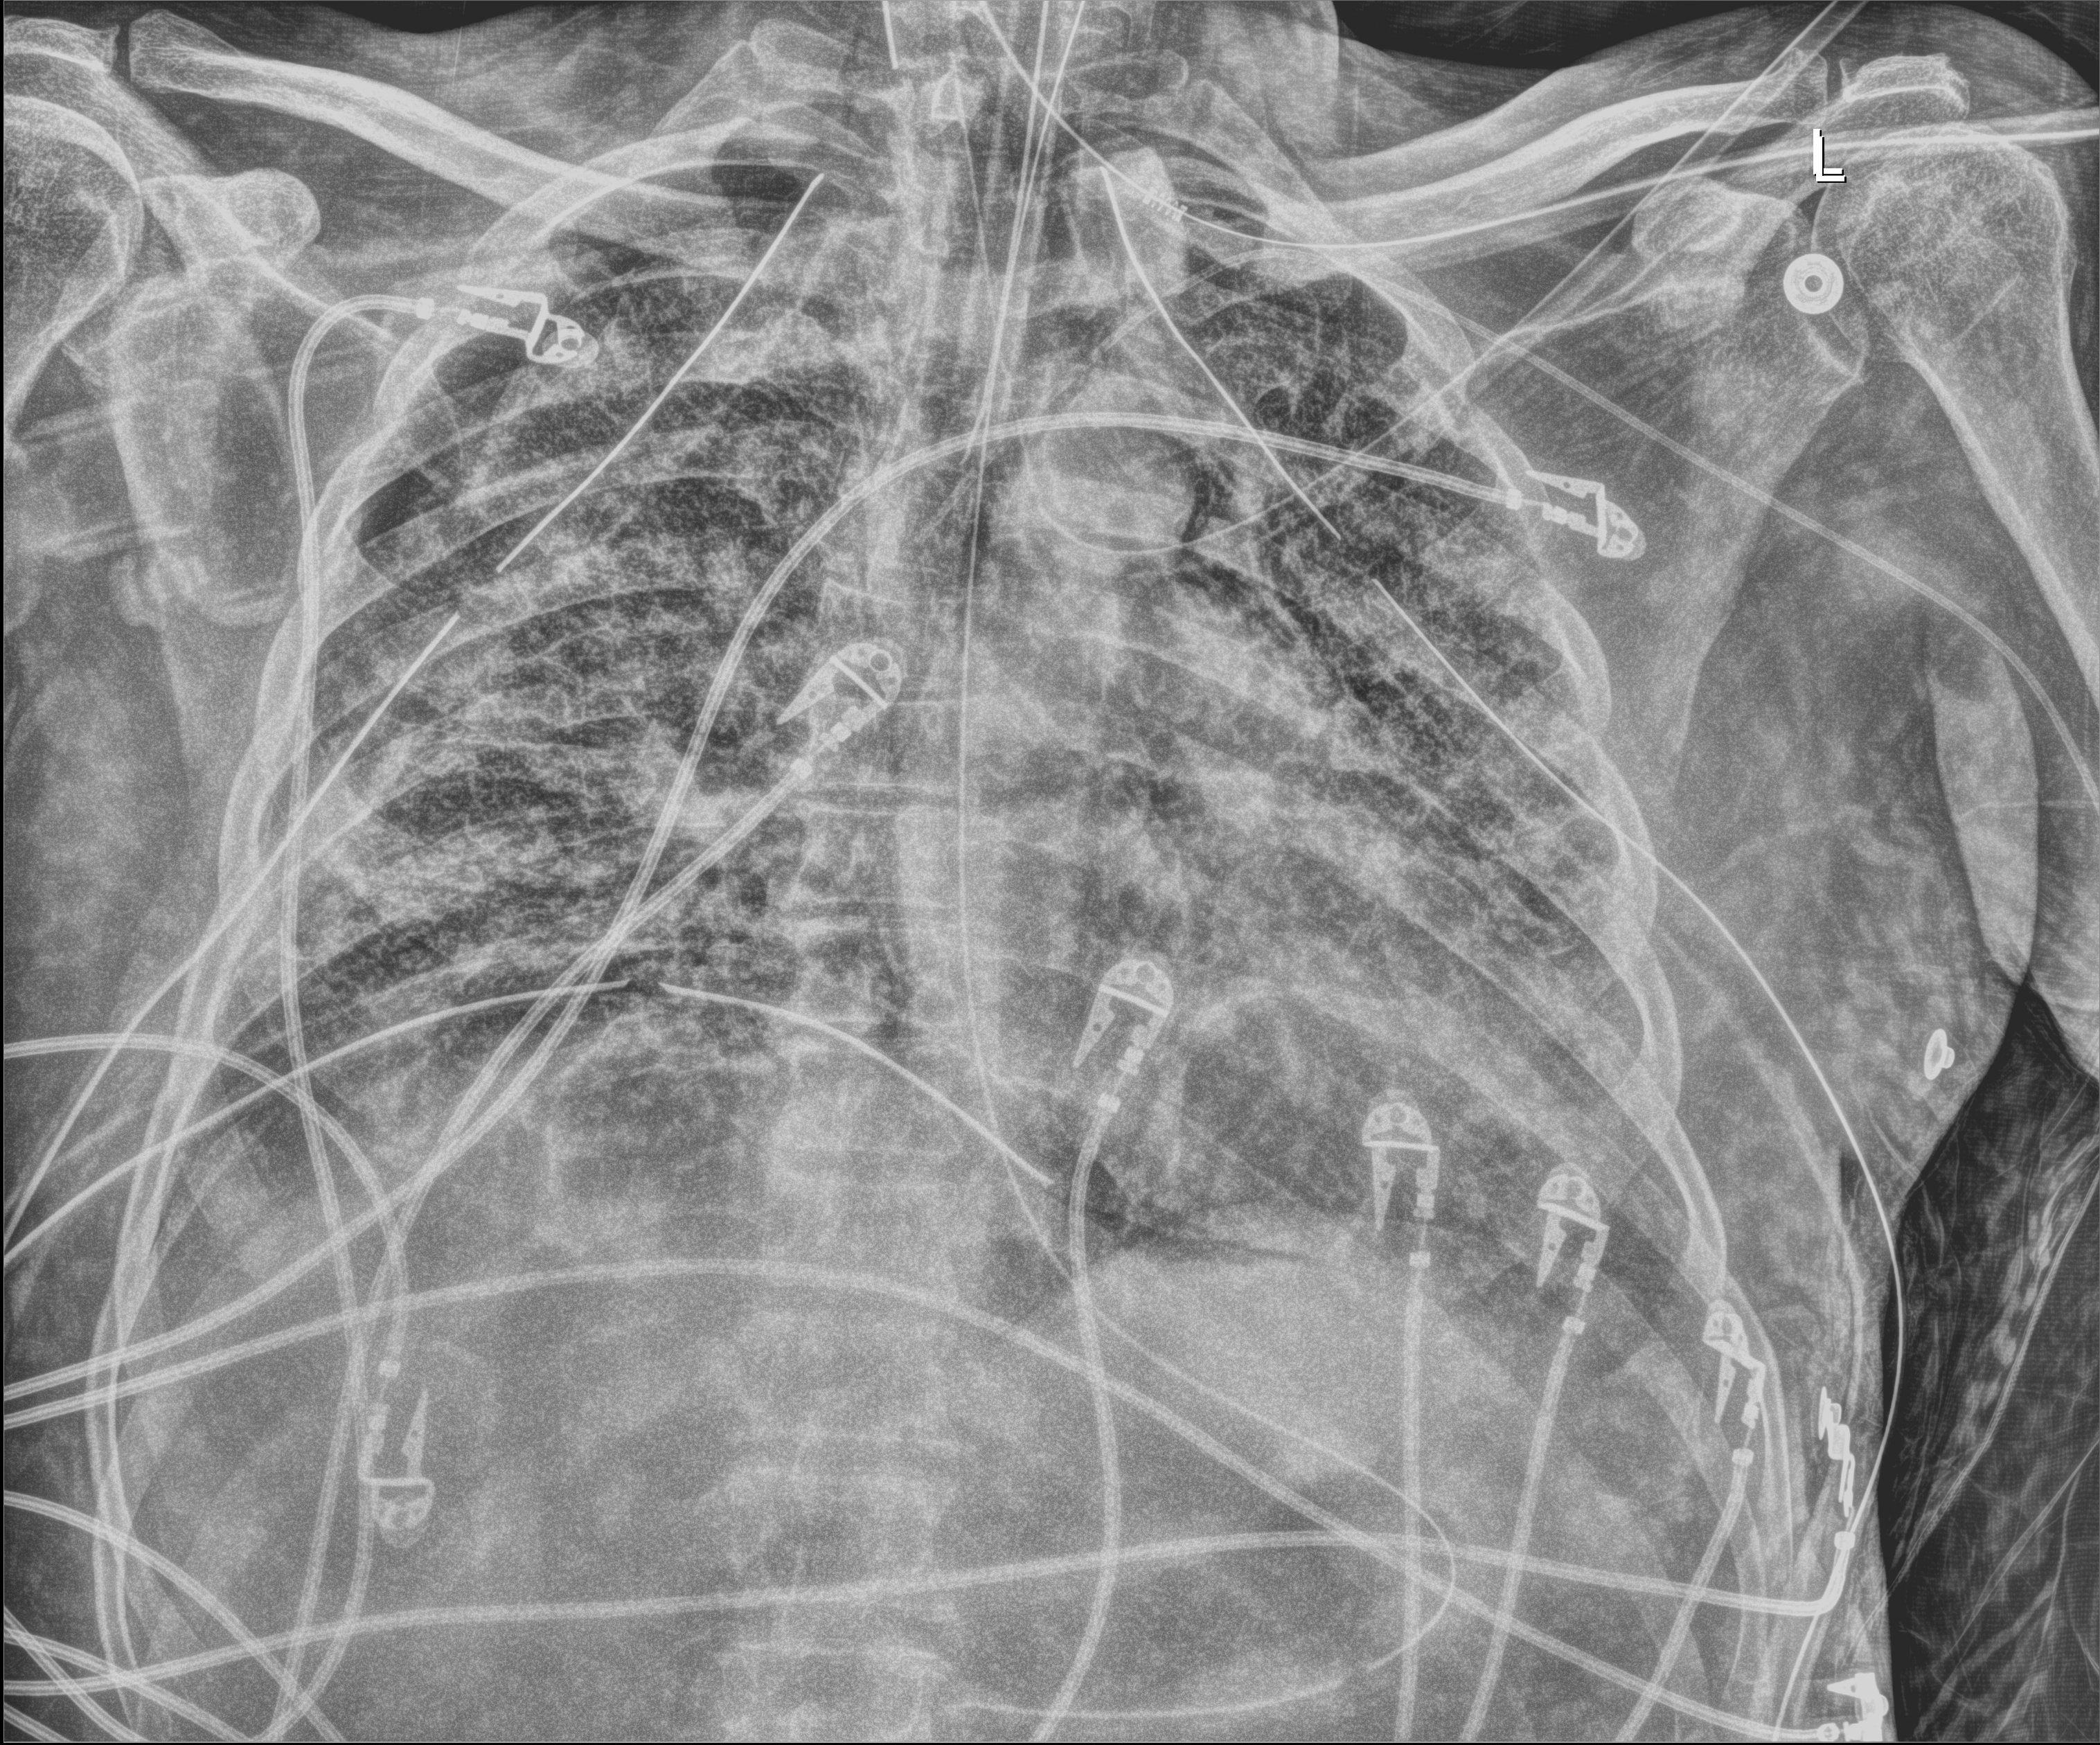
Chest X-ray (portable); anteroposterior (AP) projection. Patient hospitalised with COVID-19; male, aged 18–59 years.
From the hospital-stay record, not from the radiograph (when in the stay this image was taken is not recorded): length of hospital stay: 83 days; mechanically ventilated during this hospital stay: yes.